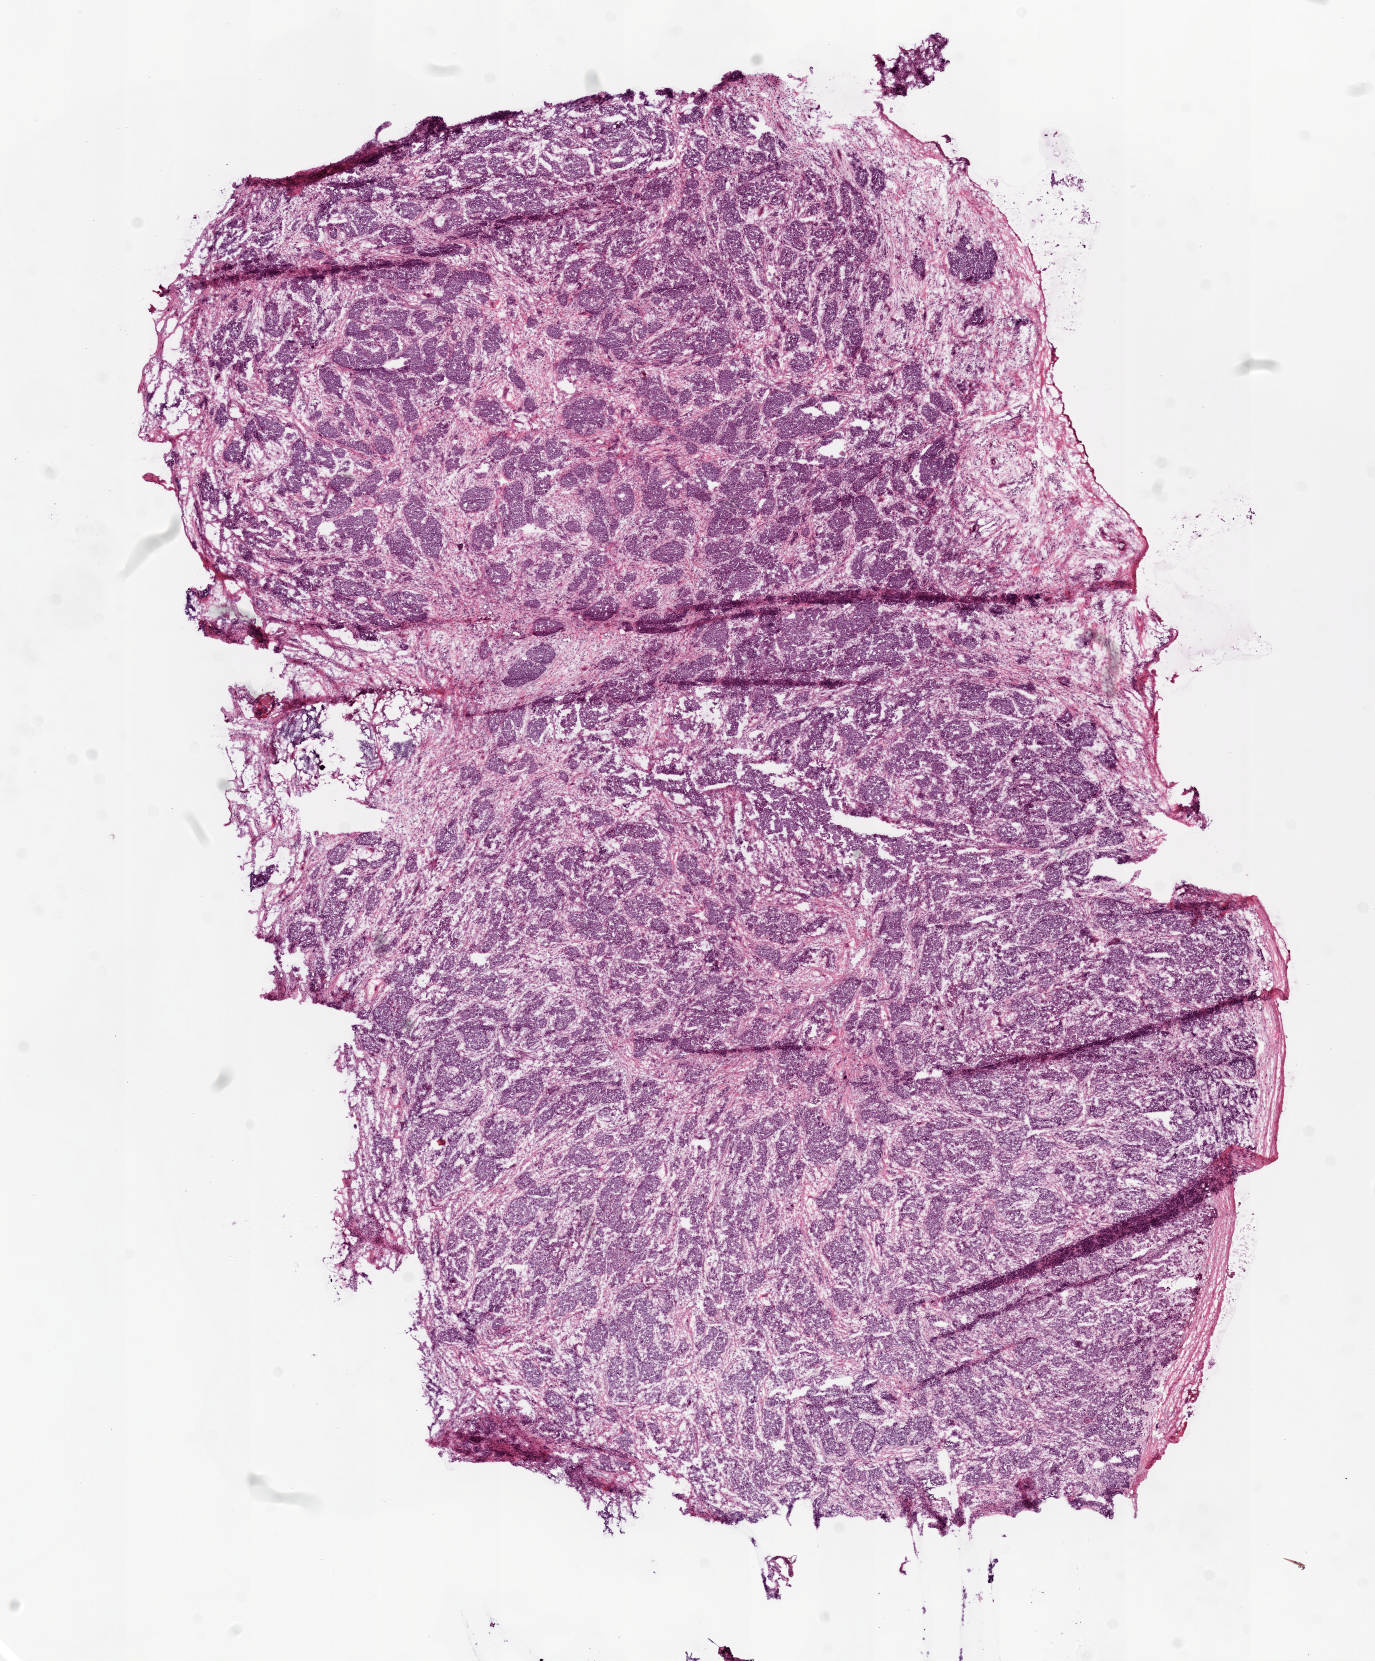
Whole-slide histology image, H&E — low-resolution overview of the scanned area, about 11.0 x 13.3 mm (from a 20x scan), frozen section from the top of the tissue portion, ovary, primary tumour sample. Female patient; age at initial diagnosis 68 years. Histologic grade: G3 (poorly differentiated). Pathologist review of this section (percent, as recorded): tumour cells 89%, tumour nuclei 90%, normal cells 0%, stromal cells 10%, necrosis 1%.
• FIGO stage: IV
• pathologic diagnosis: Serous cystadenocarcinoma, NOS